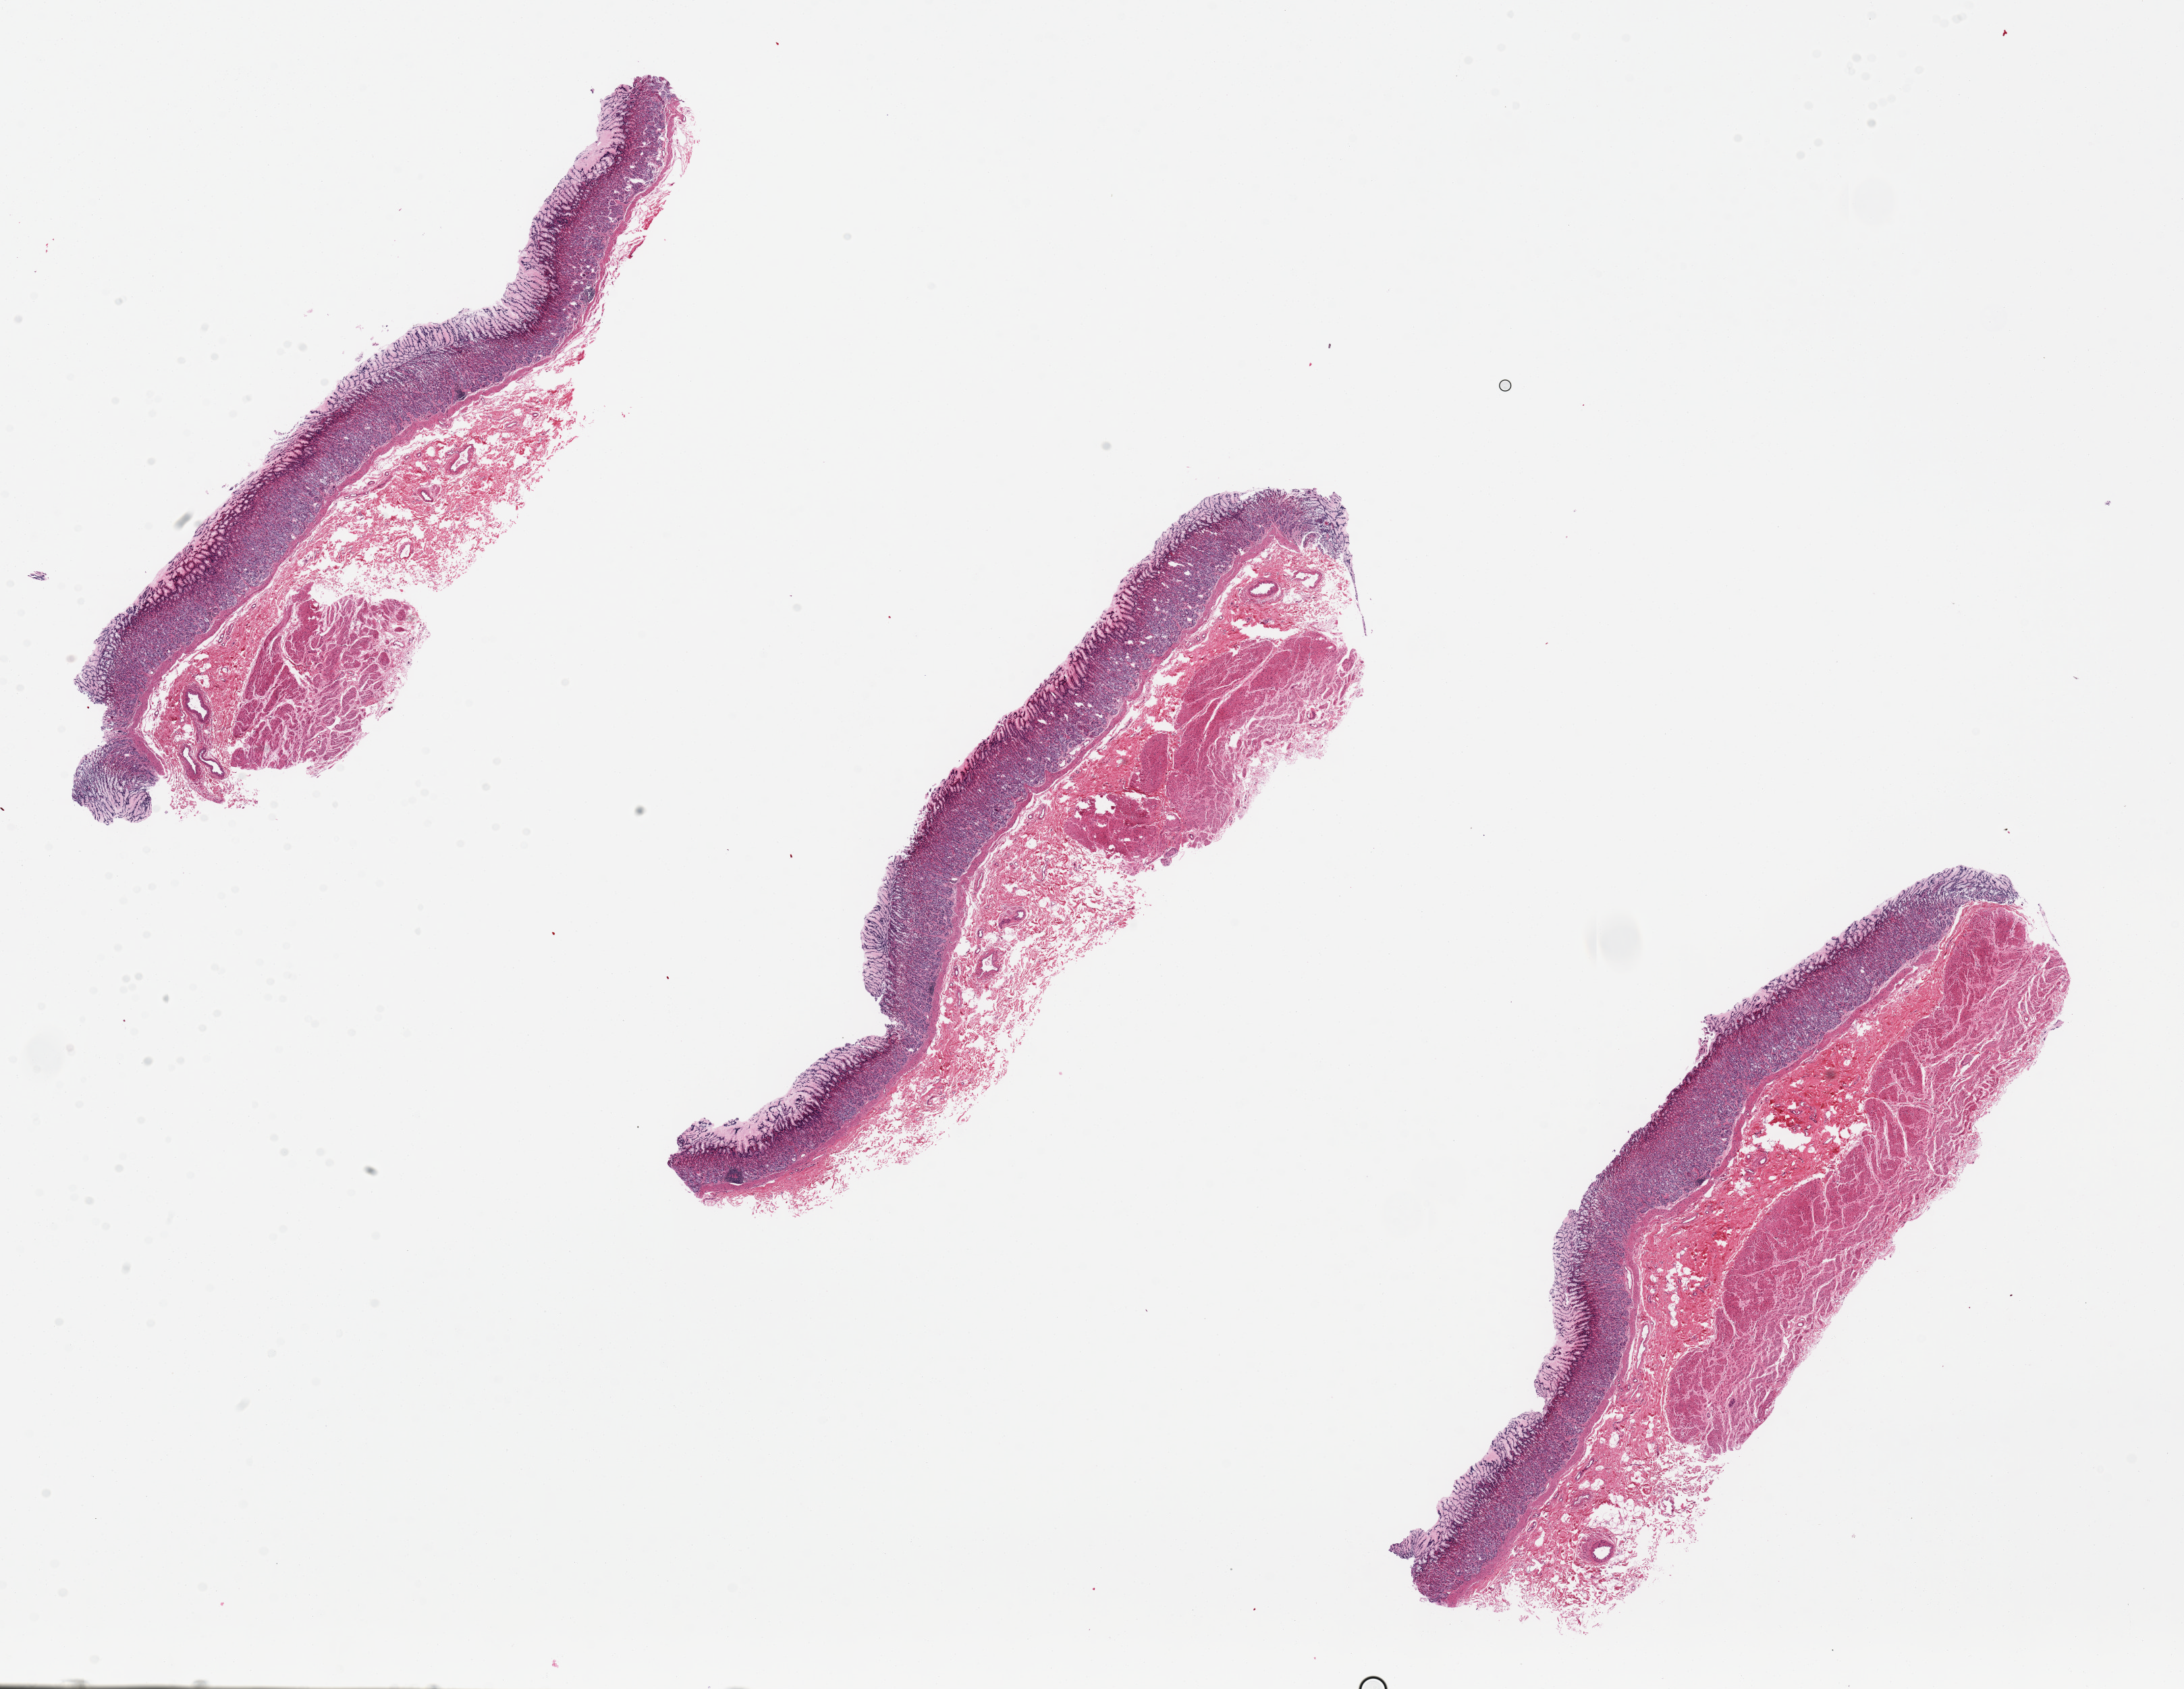
Digitized haematoxylin and eosin-stained section, low-resolution overview of the scanned area, about 25.6 x 19.8 mm. PAXgene-fixed paraffin-embedded (PFPE) section. Sampled site (target tissue): stomach. Tissue donor sample.
- reviewer comment on this tissue sample: 1, in some areas 0. Extremely well-preserved mucosa???25-30% of specimen thickness